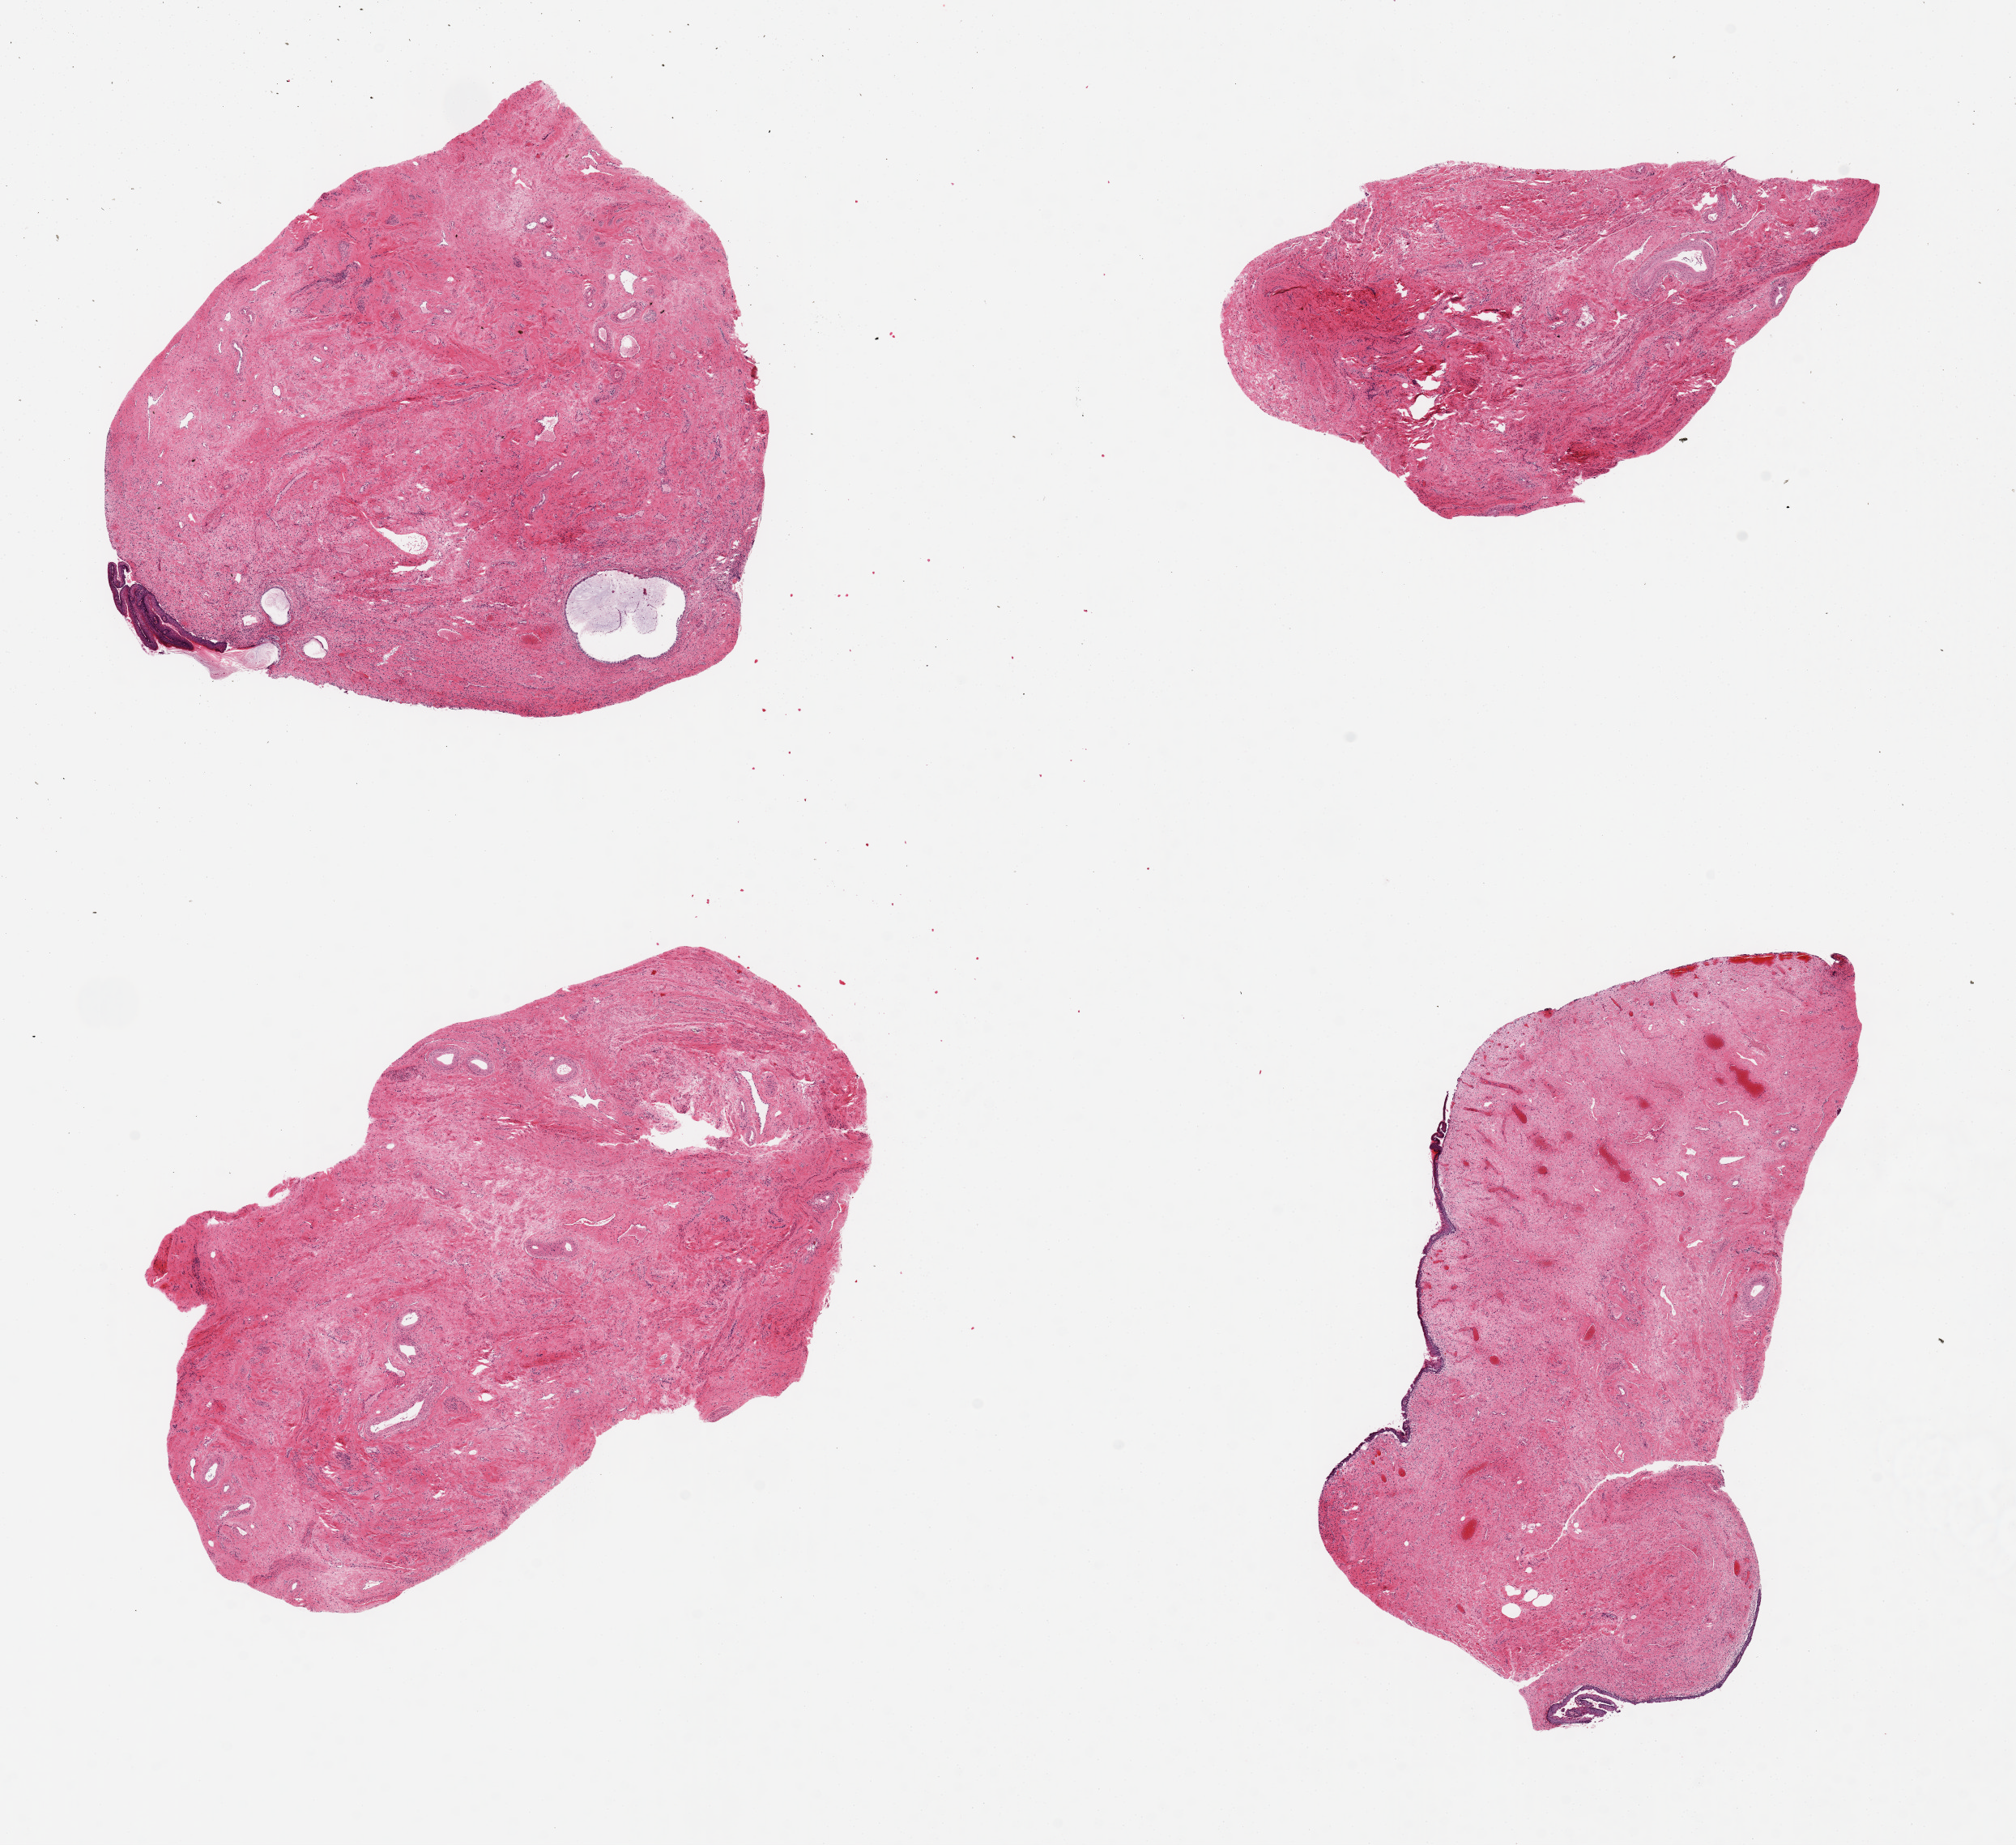
Digitized H&E-stained section, a low-resolution overview of the entire scanned area, about 19.7 x 18.0 mm; PAXgene-fixed paraffin-embedded (PFPE) section; sampled site (target tissue): exocervix; donor tissue sample. Female donor.
Pathologist's review note for this sample: 4 pieces up to 7x4 mm; squamous surface largely detached; some glands in 1 piece.